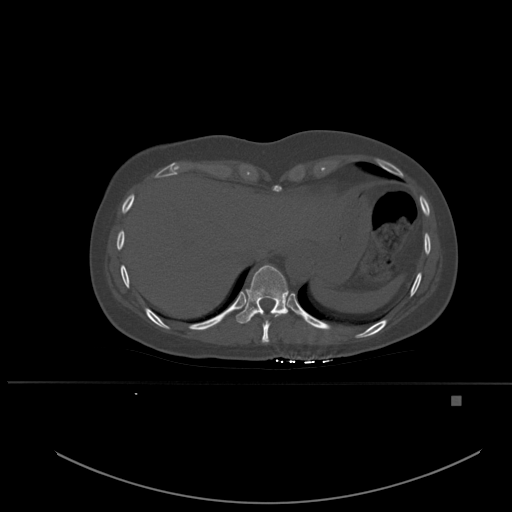
CT including the spine, one axial slice. Position 295 of 651 along the scan axis. Bone window (W 1800 / L 400 HU). 1.5 mm slice thickness. 512 × 512 image matrix, field of view 443 × 443 mm. Patient: female, 49 years. Case-level facts recorded for this patient, not image findings: primary cancer: breast; vertebrae with lytic lesions (as recorded): L3, T12, L4.
Outlined on this slice (semi-automatic segmentation, software-assisted and operator-edited):
- T10 vertebra: bounding box <236,265,289,324> (left, top, right, bottom; pixels)
- T9 vertebra: <252,312,283,343>